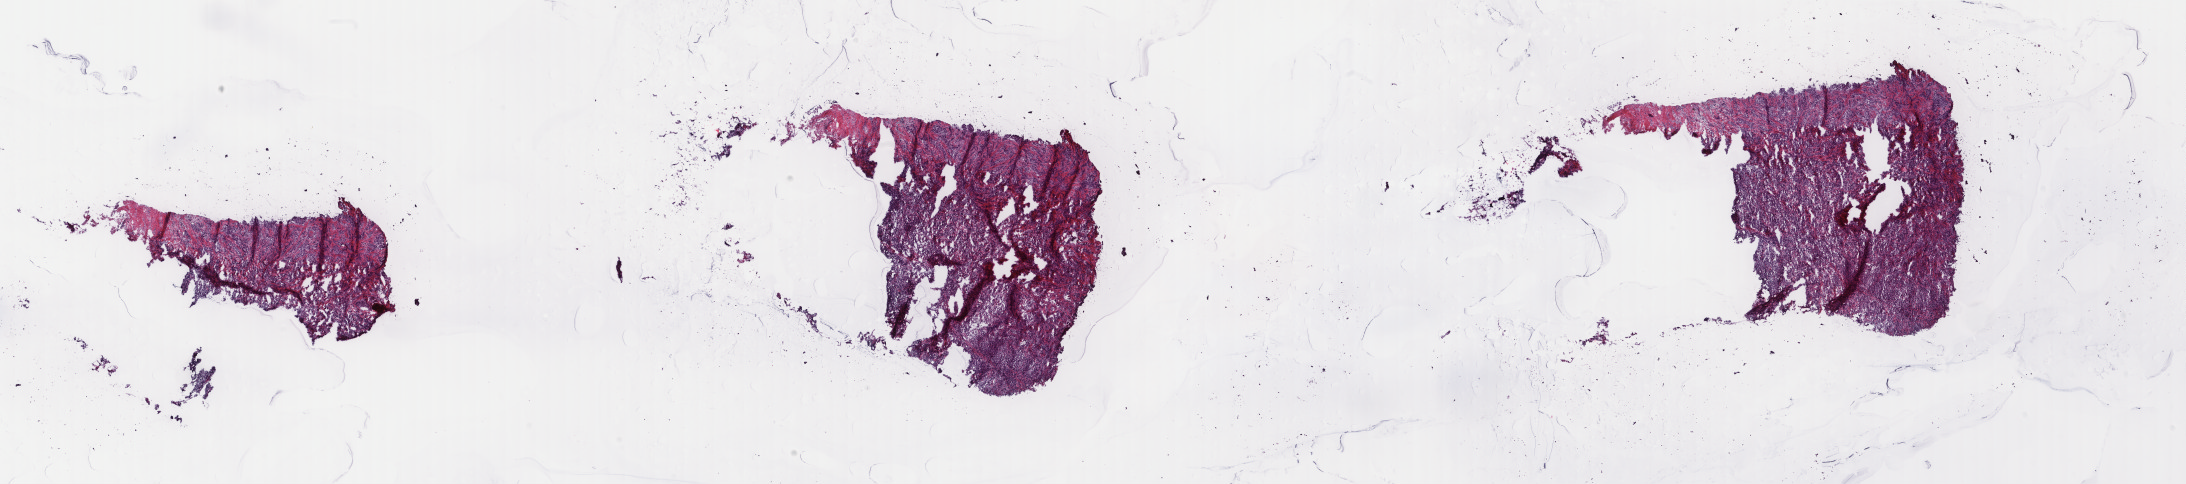
Whole-slide histology image, H&E, shown as a low-resolution overview of the whole scanned area (about 34.7 x 7.7 mm, slide scanned at 40x); frozen section from the top of the tissue portion; sample: primary tumour, breast. Female, age 79 years at initial diagnosis. Pathologist review of this section (percent, as recorded): tumour cells 100%, tumour nuclei 95%, normal cells 0%, stromal cells 0%, necrosis 0%. Inflammatory infiltration, as recorded: lymphocyte infiltration 0%, monocyte infiltration 0%, neutrophil infiltration 0%.
Pathologic diagnosis: Infiltrating duct carcinoma, NOS. AJCC pathologic stage: IIIA (7th edition). Lymph nodes positive (case pathology): 8 of 25 examined.